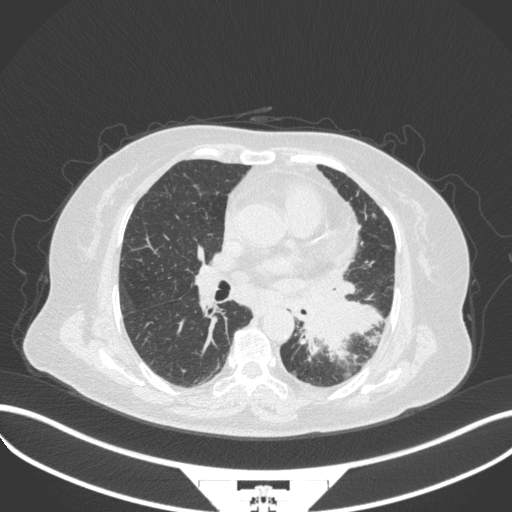
Chest CT, one axial slice. Slice 179 of 328 in the series (ordered by position). Reconstruction kernel B31f. 120 kVp. Lung window (W 1500 / L -600 HU). 1 mm slice thickness. 512 × 512 image matrix, field of view 400 × 400 mm. Female patient, age 69 years. Case-level facts recorded for this patient, not image findings: clinical TNM (as recorded): T2b N3 M1.
Annotated regions visible in this slice (rectangle marked by the reading radiologist):
- lung tumour (recorded histology: adenocarcinoma): bounding box [x1, y1, x2, y2] px = [294, 292, 387, 361]